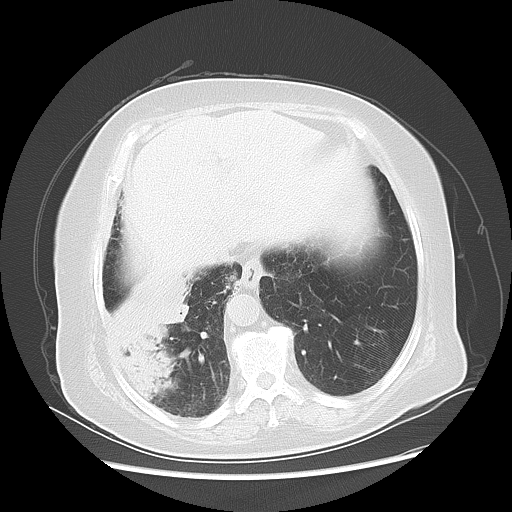
Chest CT, one axial slice; position 14 of 56 along the scan axis; 120 kVp; lung window (W 1500 / L -600 HU); 512 × 512 image matrix, field of view 378 × 378 mm. Female patient, age 73 years. From the clinical record (not read from this slice): clinical TNM (as recorded): T3 N0 M0.
Outlined on this slice (bounding box drawn by a radiologist):
- lung tumour (recorded histology: adenocarcinoma): bounding box (x1, y1, x2, y2) in pixels: (99, 272, 207, 400)